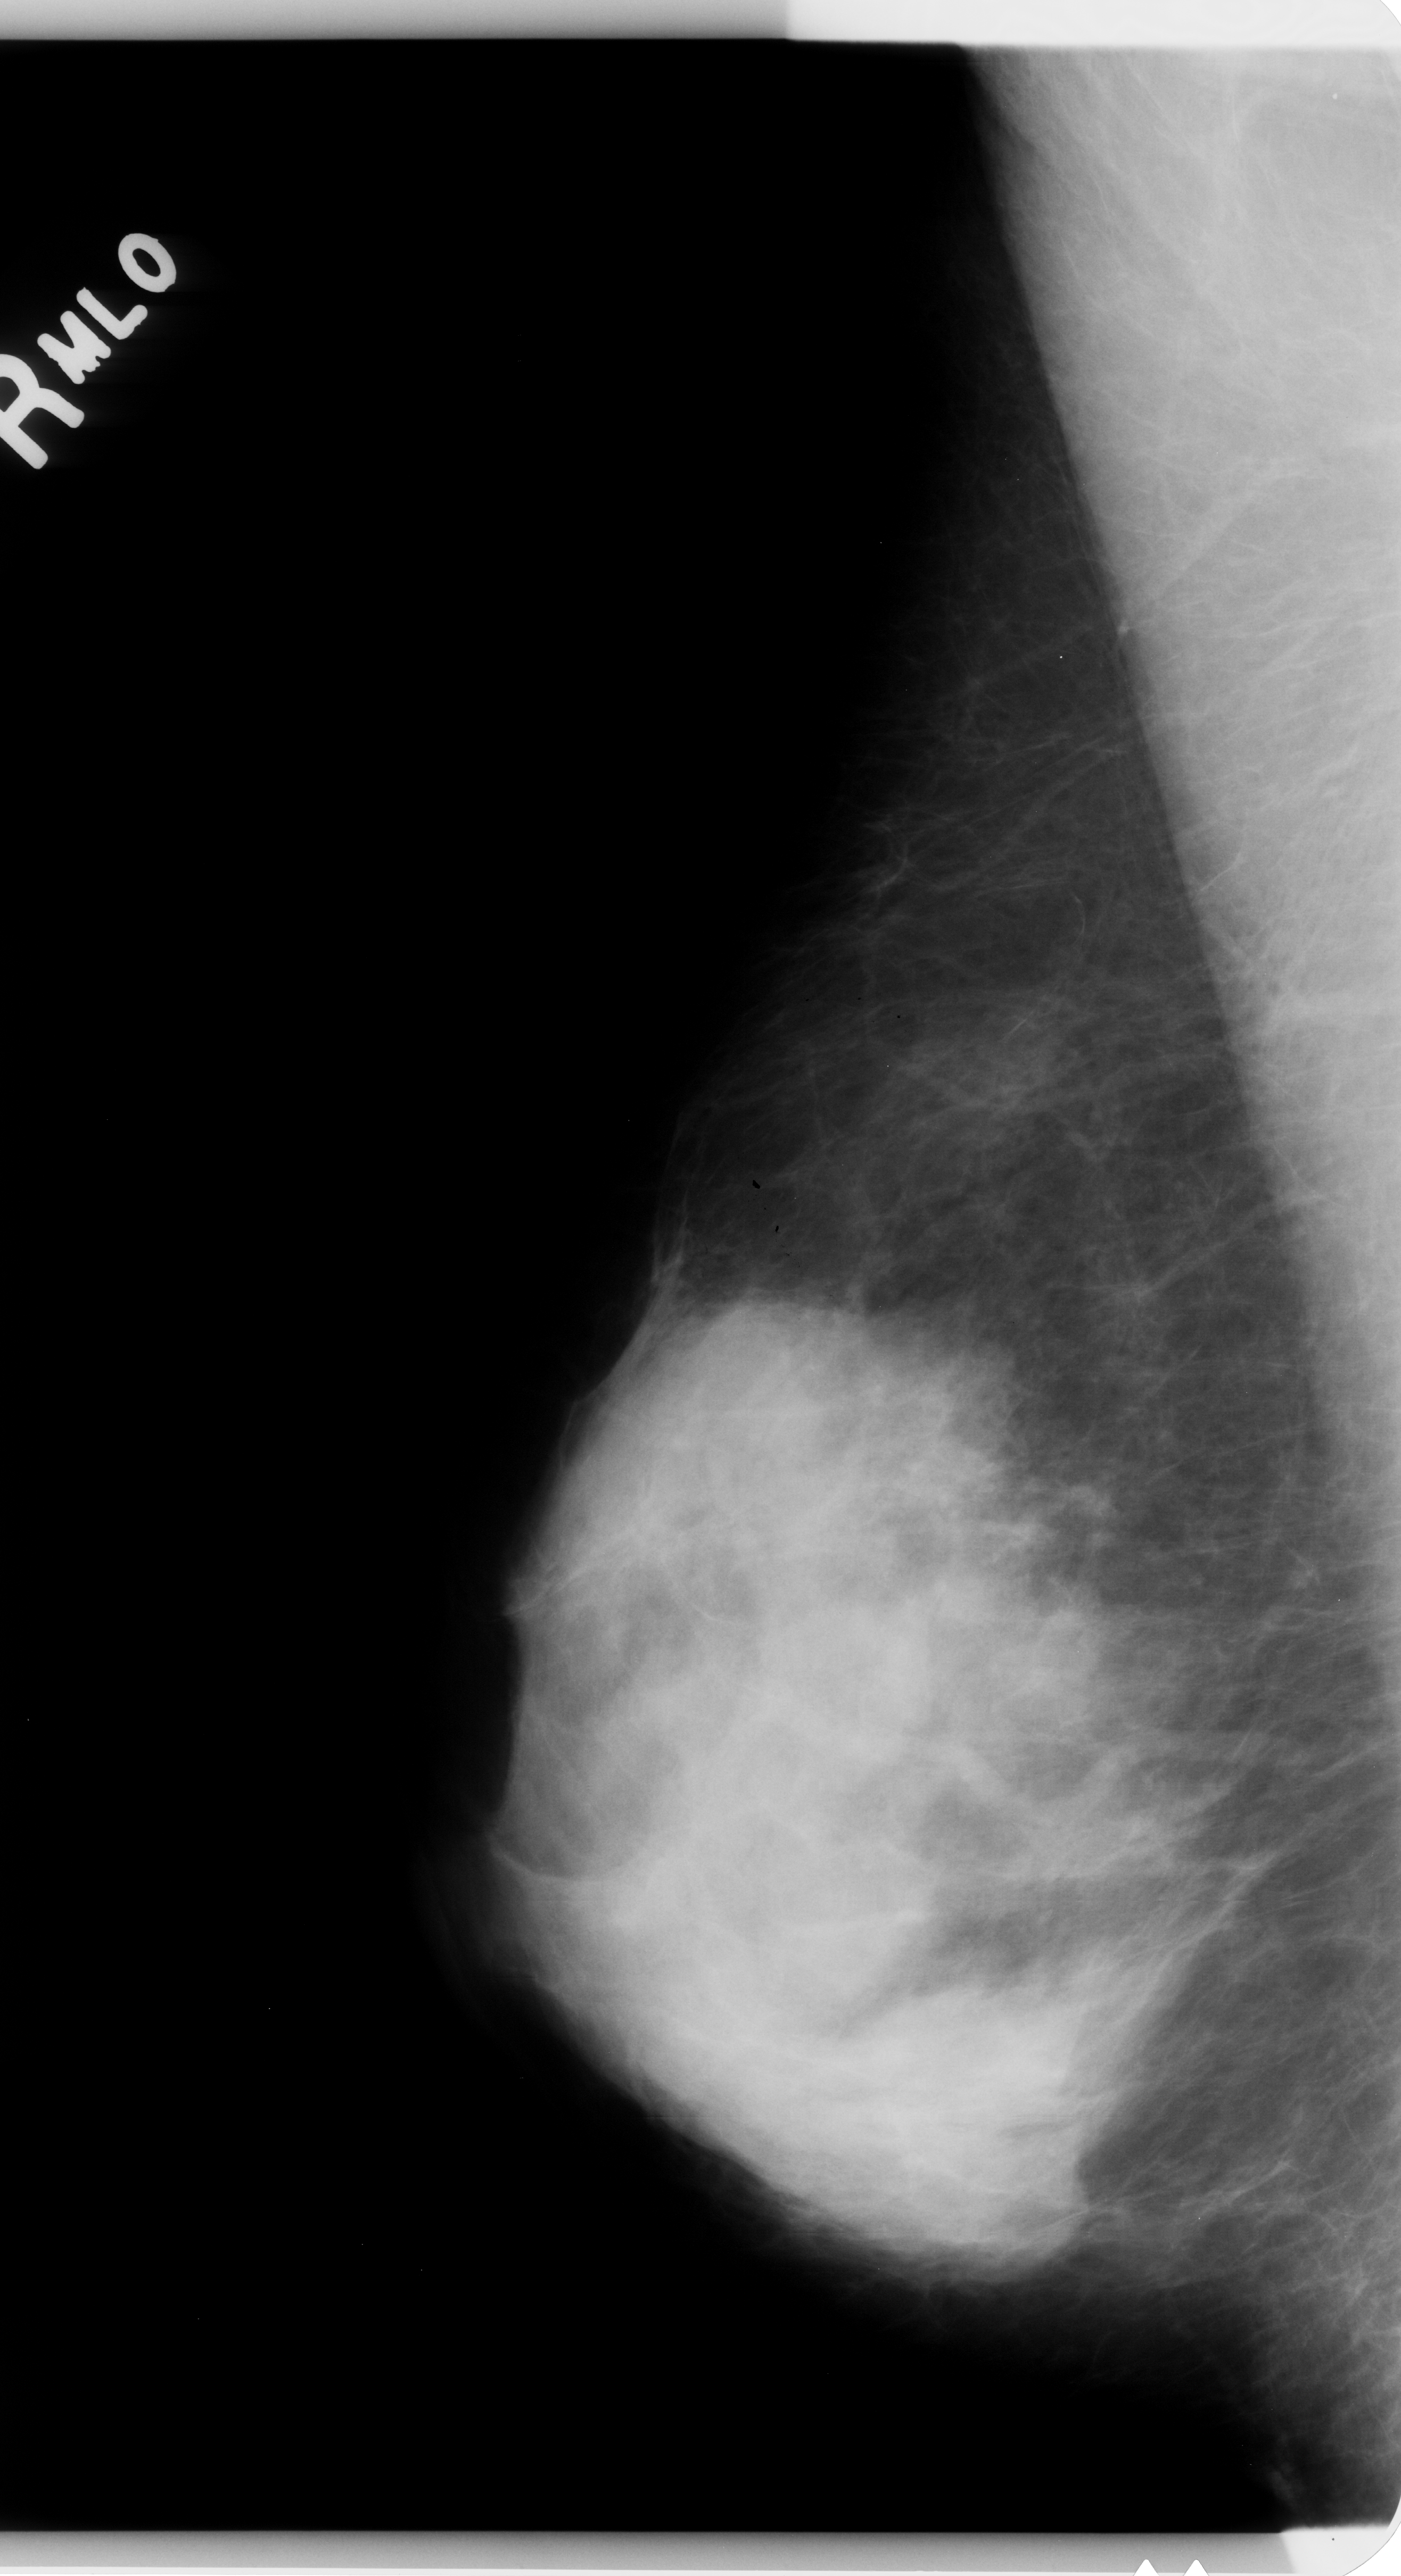
Scanned film-screen mammogram. Right breast. MLO view. 1401 × 2576 image matrix.
Marked abnormalities (boxes around the expert regions of interest):
- mass, shape oval, margins obscured; BI-RADS assessment category 3; pathology (as recorded): benign: box from (x=771, y=1859) to (x=963, y=2020) px